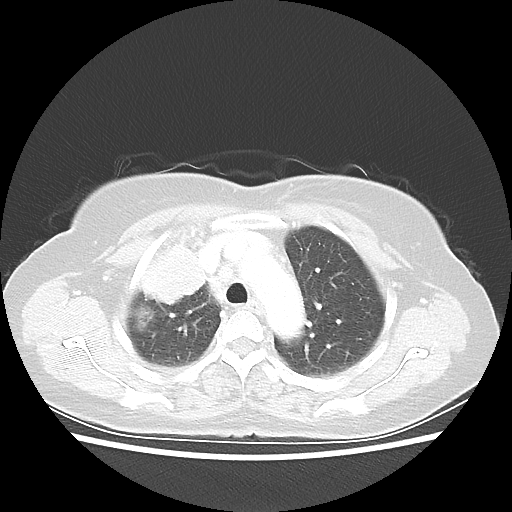
Chest CT, one axial slice. Position 41 of 55 along the scan axis. 80 kVp. Lung window (W 1500 / L -600 HU). 5 mm slice thickness. 512 × 512 image matrix, field of view 337 × 337 mm. Patient: female, 62 years. Case-level facts recorded for this patient, not image findings: clinical TNM (as recorded): T4 N3 M0.
Annotated regions visible in this slice (rectangle marked by the reading radiologist):
- lung tumour (recorded histology: squamous cell carcinoma): bounding box <129,238,213,306> (left, top, right, bottom; pixels)